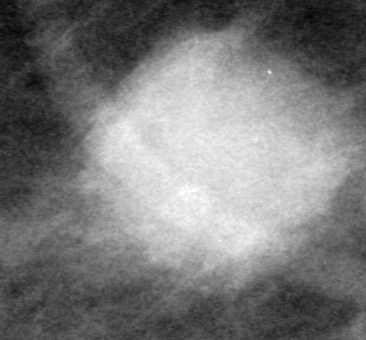
Cropped region of a digitized screen-film mammogram centred on a radiologist-marked abnormality; right breast; MLO view.
Marked abnormality: mass, shape round, margins ill defined; BI-RADS assessment category 5; subtlety rating 5 on a 1 (subtle) to 5 (obvious) scale; pathology (as recorded): malignant.